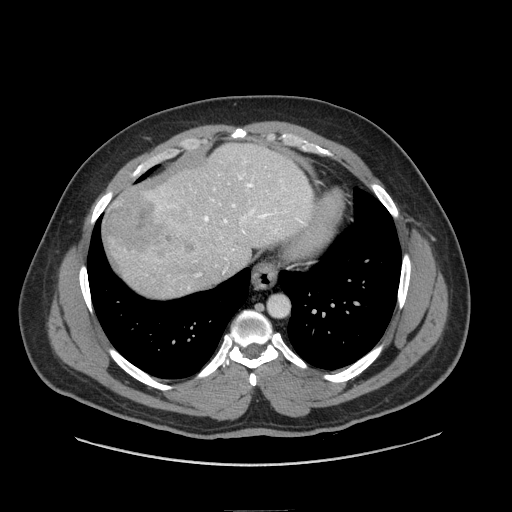
Contrast-enhanced abdominal CT (liver protocol), one axial slice; position 68 of 87 along the scan axis; reconstruction kernel STANDARD; 140 kVp; soft-tissue window (W 400 / L 40 HU); 2.5 mm slice thickness; 512 × 512 image matrix. Case-level facts recorded for this patient, not image findings: diagnosis: hepatocellular carcinoma (patient treated with transarterial chemoembolisation; whether this scan precedes or follows treatment is not stated here); TNM stage (as recorded): Stage-II; Child-Pugh class: A; tumour differentiation: moderately differentiated; tumour nodularity: uninodular.
Annotated regions visible in this slice (semi-automatic segmentation, software-assisted and operator-edited):
- liver parenchyma outside the tumour (the mass and vessels are separate outlines, so this box may not span the whole liver): bounding box <104,144,312,298> (left, top, right, bottom; pixels)
- mass: <103,187,193,270>
- liver vessels: <158,161,303,276>